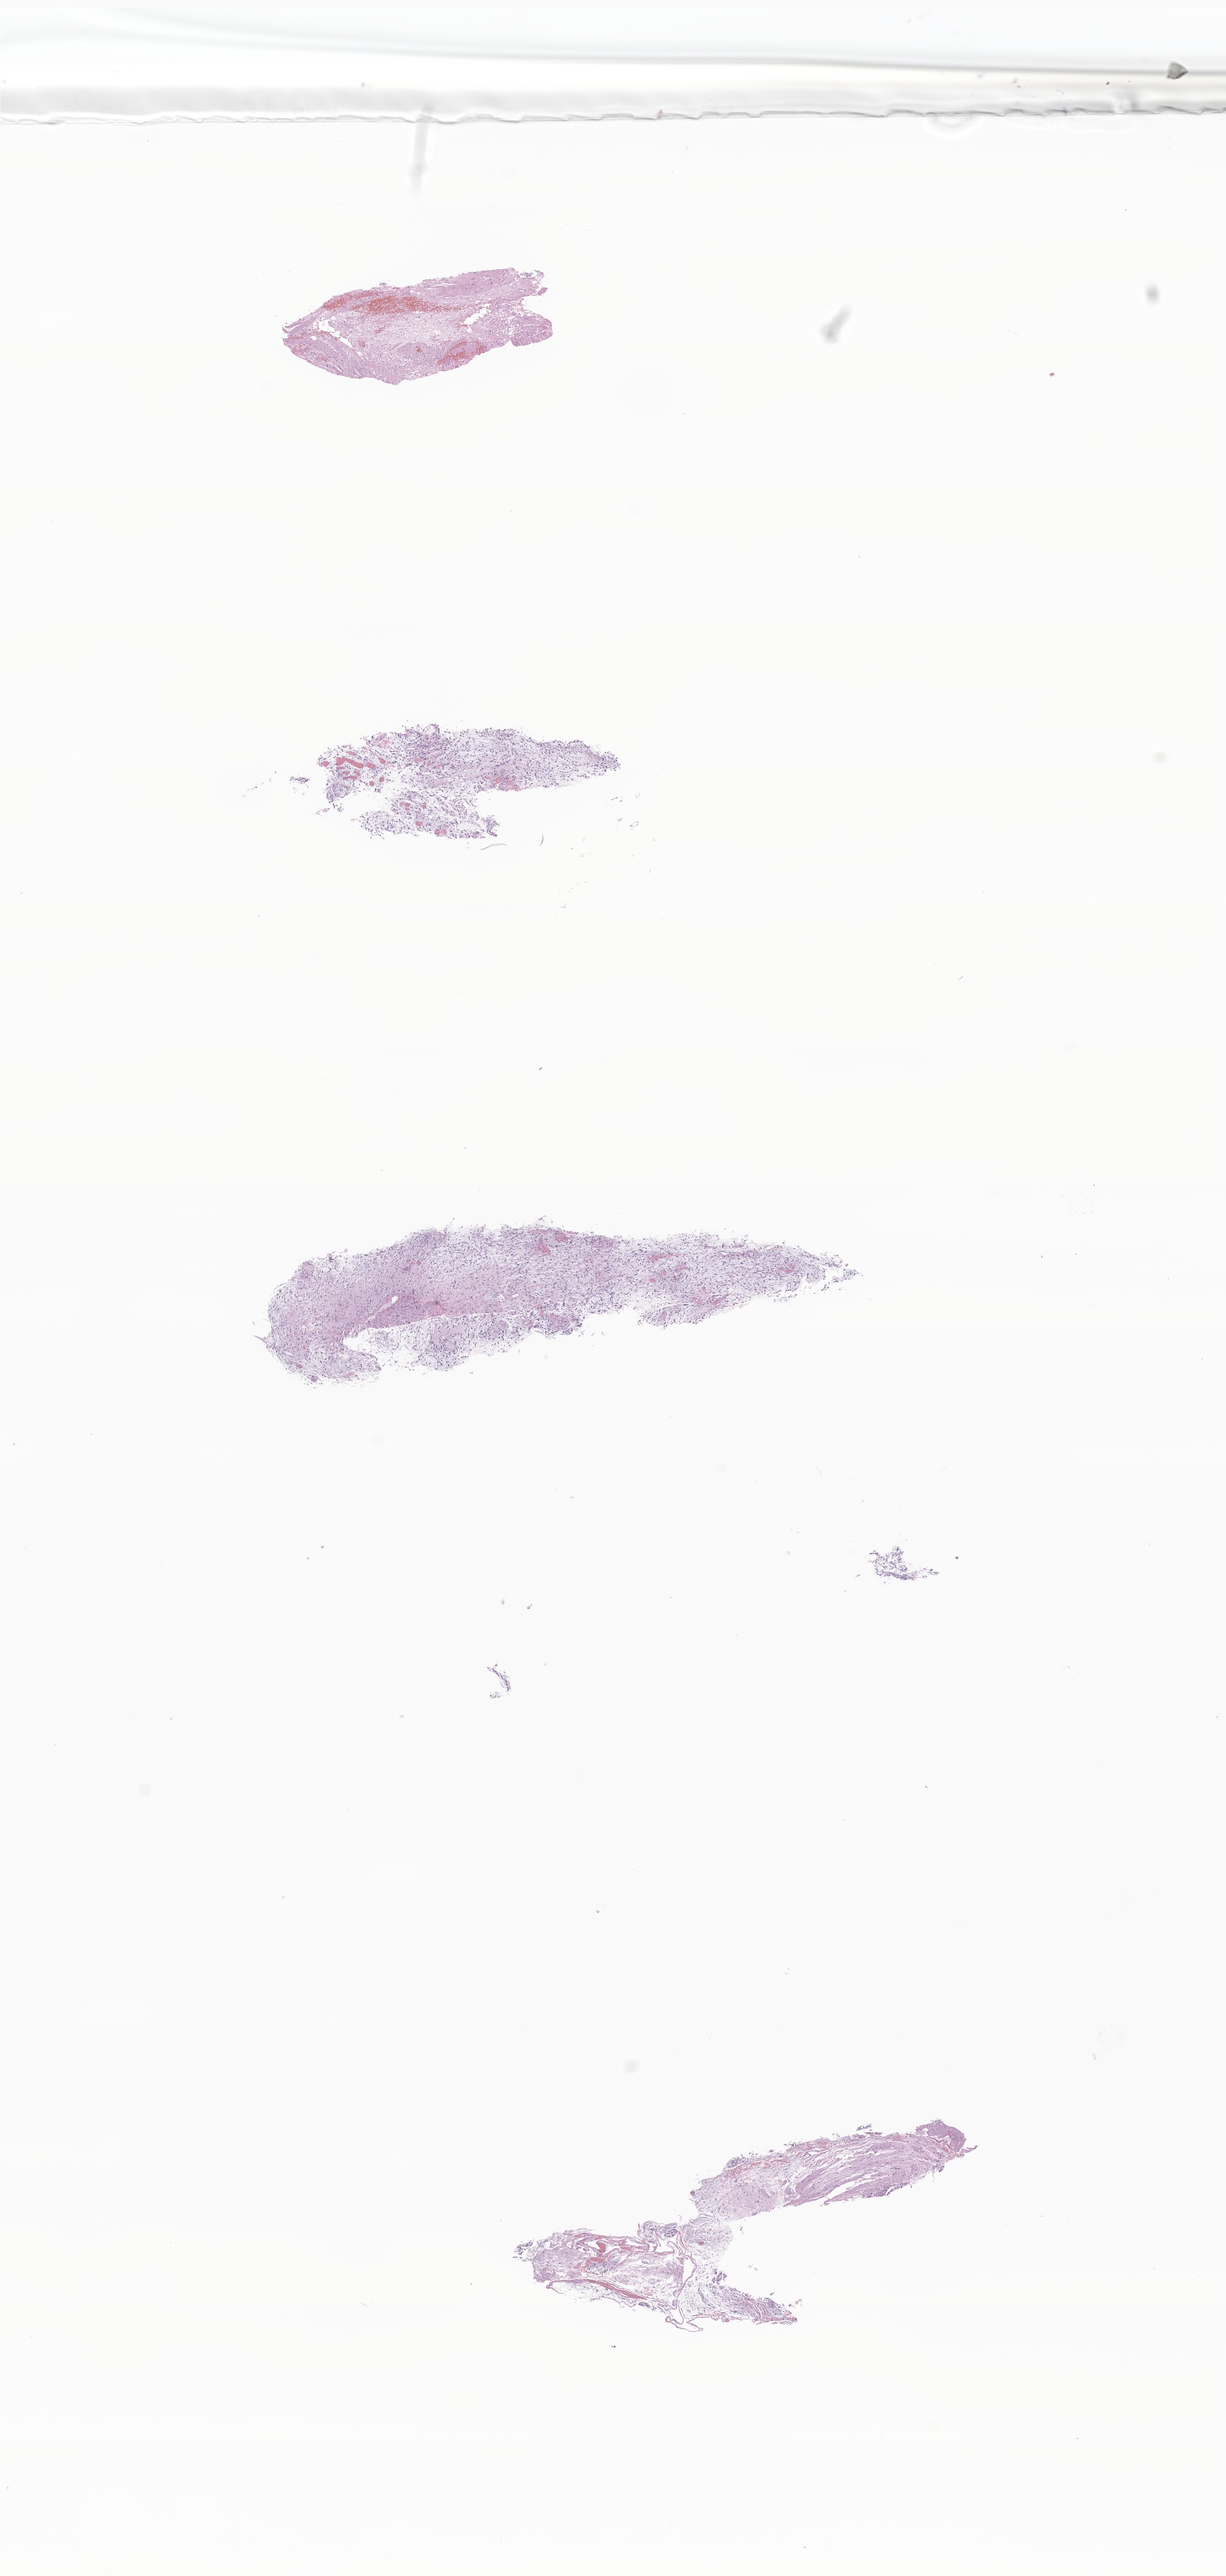
Whole-slide image, haematoxylin and eosin stain of tumor tissue from the brain — a low-resolution overview of the entire scanned area, about 9.3 x 19.6 mm; FFPE section. Patient male; age 103 months.
Diagnosis: Pilocytic astrocytoma.